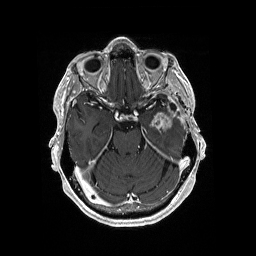
Brain MRI from a brain-tumour surgery series, one axial slice. Slice 120 of 176 in the series (ordered by position). T1-weighted post-contrast. 256 × 256 image matrix, field of view 256 × 256 mm. From the clinical record (not read from this slice): histopathology: Glioblastoma; WHO grade: 4; IDH mutation: no; tumour location: Left Medial Temporal.
Outlined on this slice (manually delineated by an expert):
- previous resection cavity: bounding box [x1, y1, x2, y2] px = [170, 104, 176, 109]
- tumour: [149, 112, 174, 132]